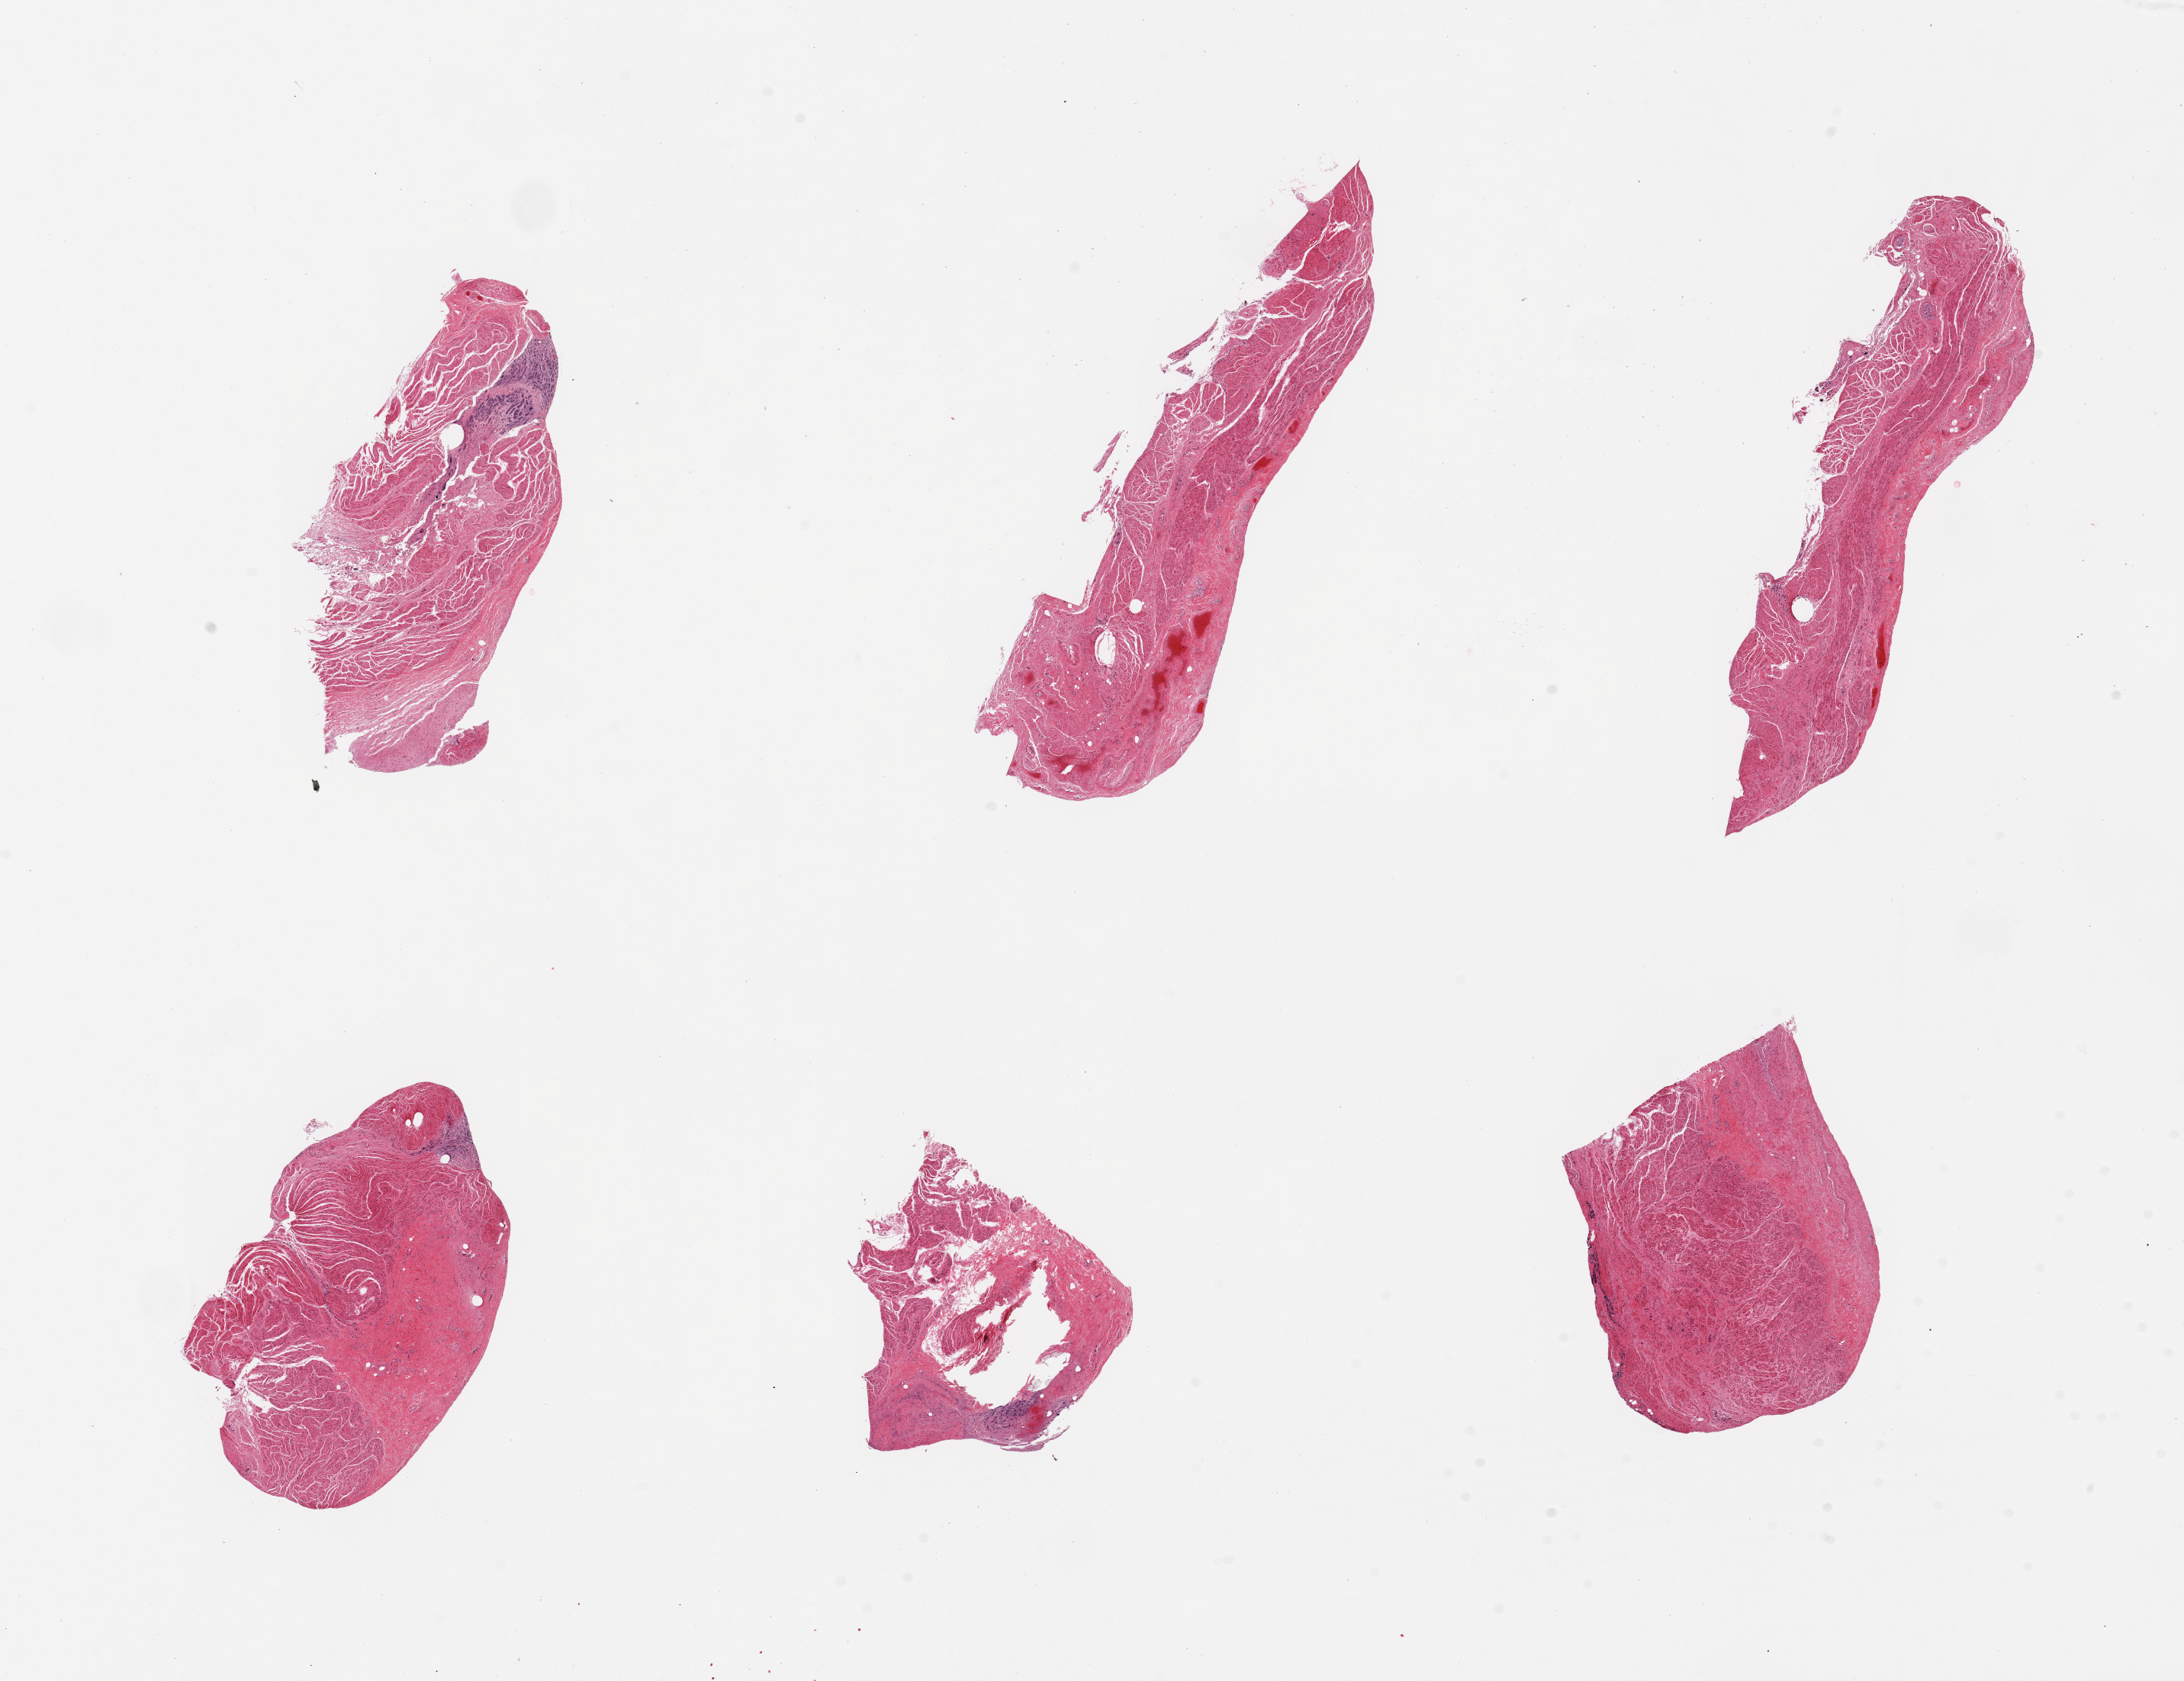
Whole-slide image, H&E stain, low-resolution overview of the scanned area, about 22.6 x 17.4 mm (acquisition: 20x scan). PAXgene-fixed, paraffin-embedded tissue. Sampled site (target tissue): gastroesophageal junction. Tissue donor sample. Donor: female.
* review note (as recorded): 6 pieces; predominantly muscularis, but with few strips of autolyzed gastric mucosa (<10%)